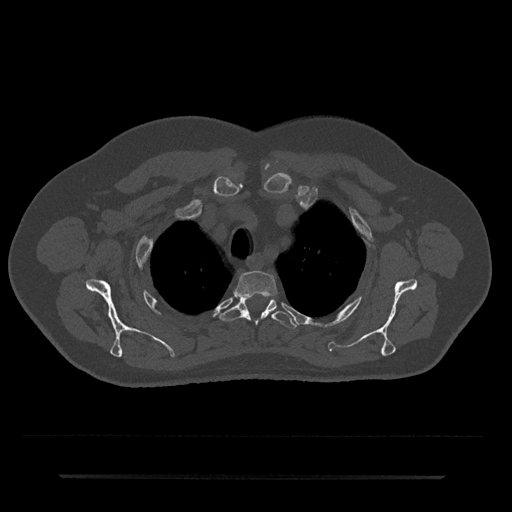
CT including the spine, one axial slice; slice 581 of 797 in the series (ordered by position); 120 kVp; bone window (W 1800 / L 400 HU); 0.5 mm slice thickness; 512 × 512 image matrix, field of view 437 × 437 mm. Patient: male, 69 years. Case-level facts recorded for this patient, not image findings: primary cancer: prostate.
Structures marked on this image (semi-automatically segmented with operator editing):
- T2 vertebra: box from (x=235, y=271) to (x=277, y=298) px
- T3 vertebra: (x=221, y=297)–(x=298, y=329)